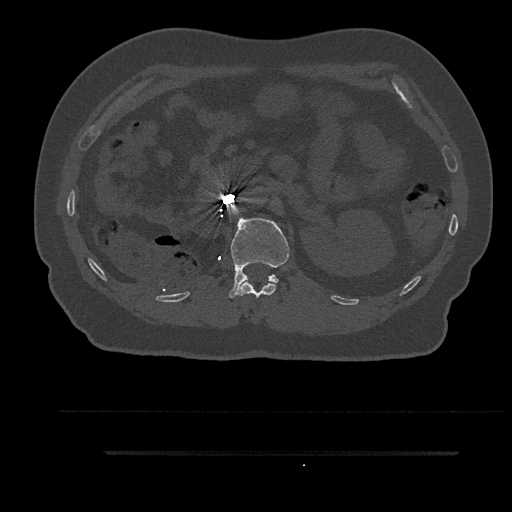
CT including the spine, one axial slice. Position 198 of 797 along the scan axis. Reconstruction kernel Br40s/3. Bone window (W 1800 / L 400 HU). 0.5 mm slice thickness. 512 × 512 image matrix, field of view 432 × 432 mm. Patient: male, 63 years. From the clinical record (not read from this slice): primary cancer: renal; vertebrae with lytic lesions (as recorded): T8.
Outlined on this slice (semi-automatically segmented with operator editing):
- L1 vertebra: bounding box (x1, y1, x2, y2) in pixels: (229, 218, 290, 298)
- T12 vertebra: (239, 281, 276, 298)